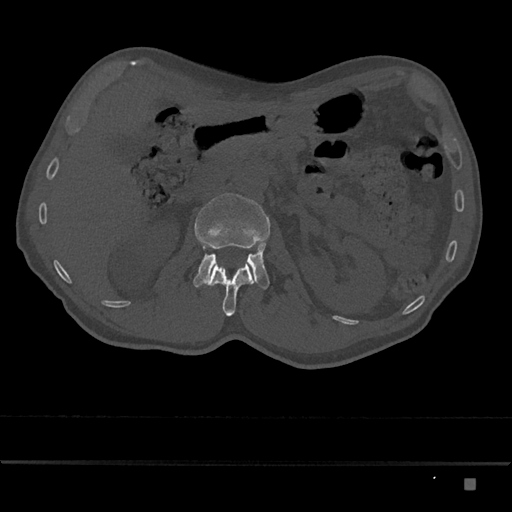
CT including the spine, one axial slice. Slice 510 of 797 in the series (ordered by position). 120 kVp. Bone window (W 1800 / L 400 HU). 0.5 mm slice thickness. 512 × 512 image matrix, field of view 390 × 390 mm. Patient: male, 72 years. From the clinical record (not read from this slice): primary cancer: prostate.
Structures marked on this image (semi-automatic segmentation, software-assisted and operator-edited):
- L1 vertebra: bounding box (x1, y1, x2, y2) in pixels: (206, 263, 255, 316)
- L2 vertebra: (193, 193, 270, 289)